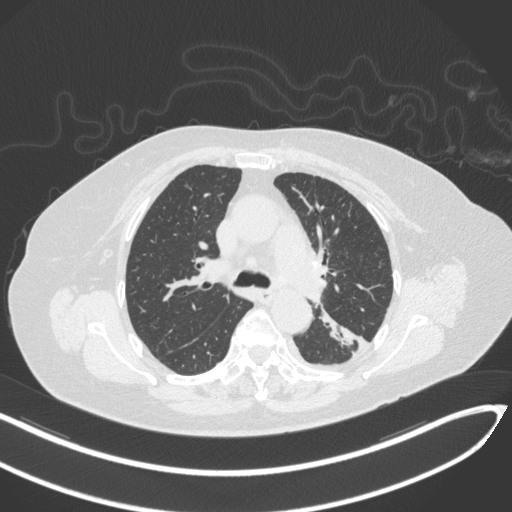
Chest CT, one axial slice. Slice 206 of 270 in the series (ordered by position). 120 kVp. Lung window (W 1500 / L -600 HU). 1 mm slice thickness. 512 × 512 image matrix, field of view 400 × 400 mm. Female patient, age 76 years. Case-level facts recorded for this patient, not image findings: clinical TNM (as recorded): T1c N0 M0.
Structures marked on this image (bounding box drawn by a radiologist):
- lung tumour (recorded histology: adenocarcinoma): bounding box (x1, y1, x2, y2) in pixels: (319, 309, 356, 350)